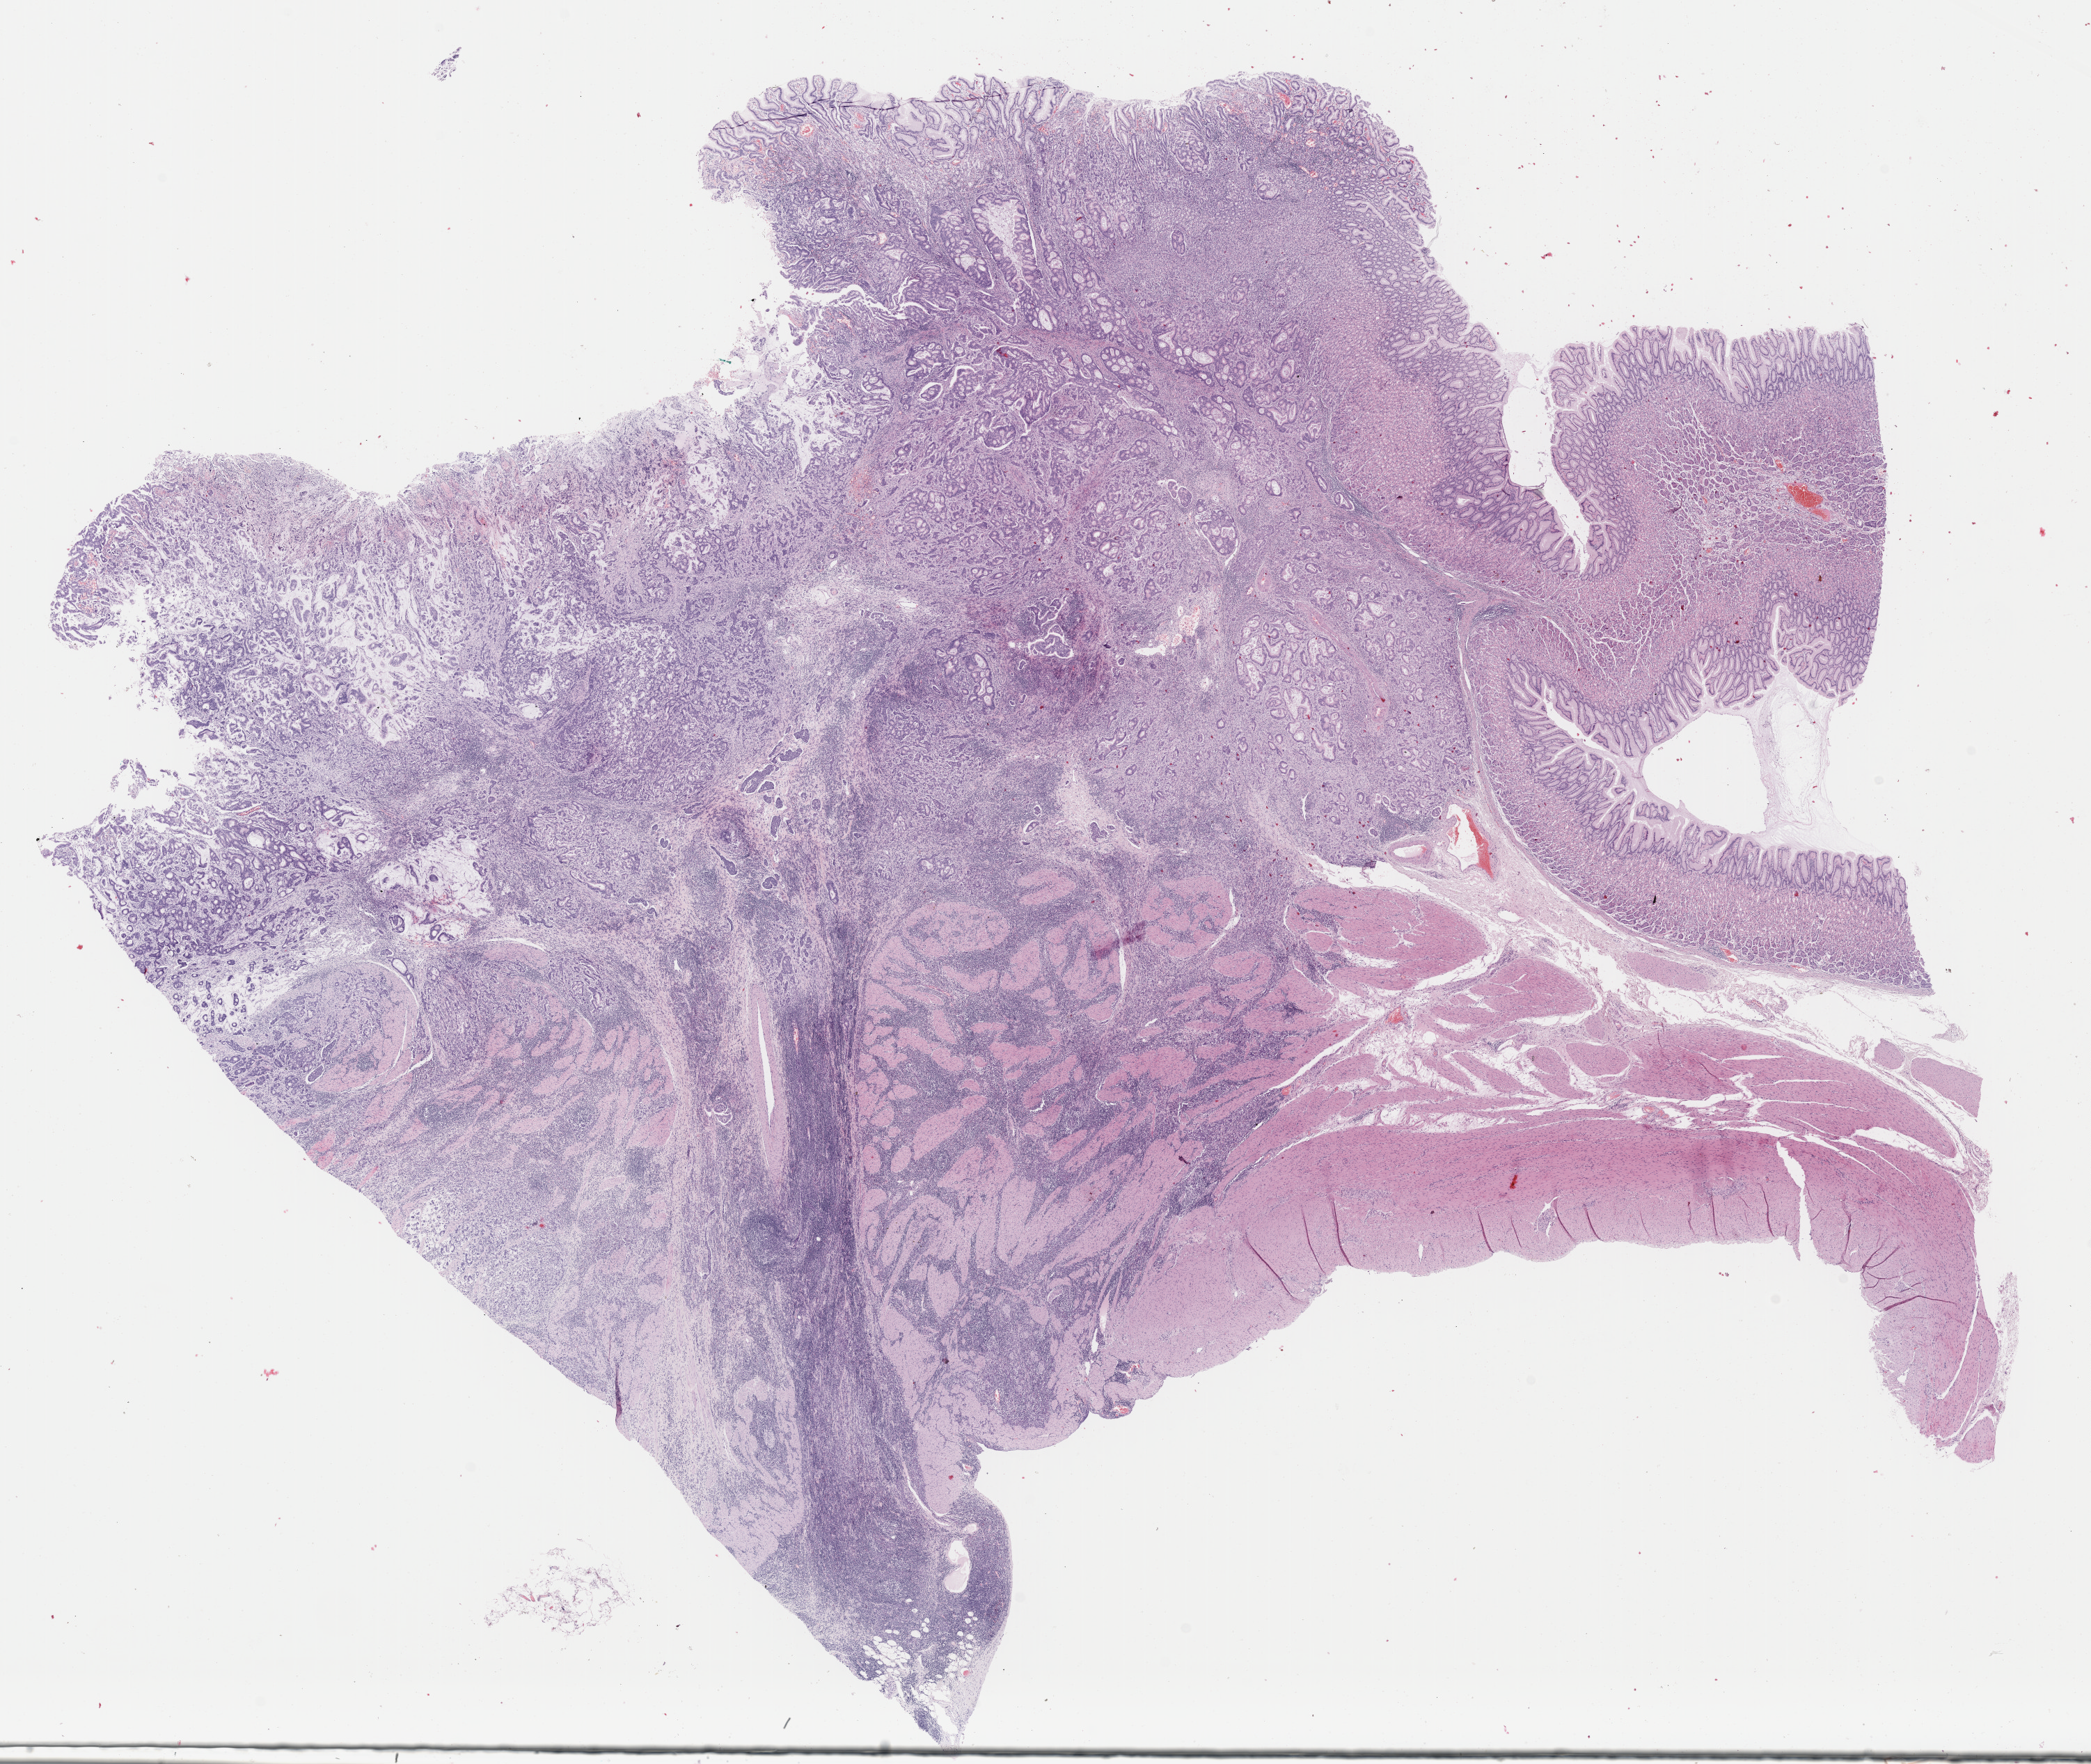
H&E whole-slide image, whole scanned area (about 23.7 x 20.0 mm, from a 40x scan) shown as a low-resolution overview; formalin-fixed paraffin-embedded (FFPE) diagnostic section; primary tumour sample from the stomach. Female patient; age at initial diagnosis 69 years. Histologic grade: G3 (poorly differentiated).
Histologic diagnosis: Tubular adenocarcinoma (gastric antrum). AJCC pathologic stage: IIB (7th edition). Lymph nodes positive (case pathology): 2 of 8 examined.